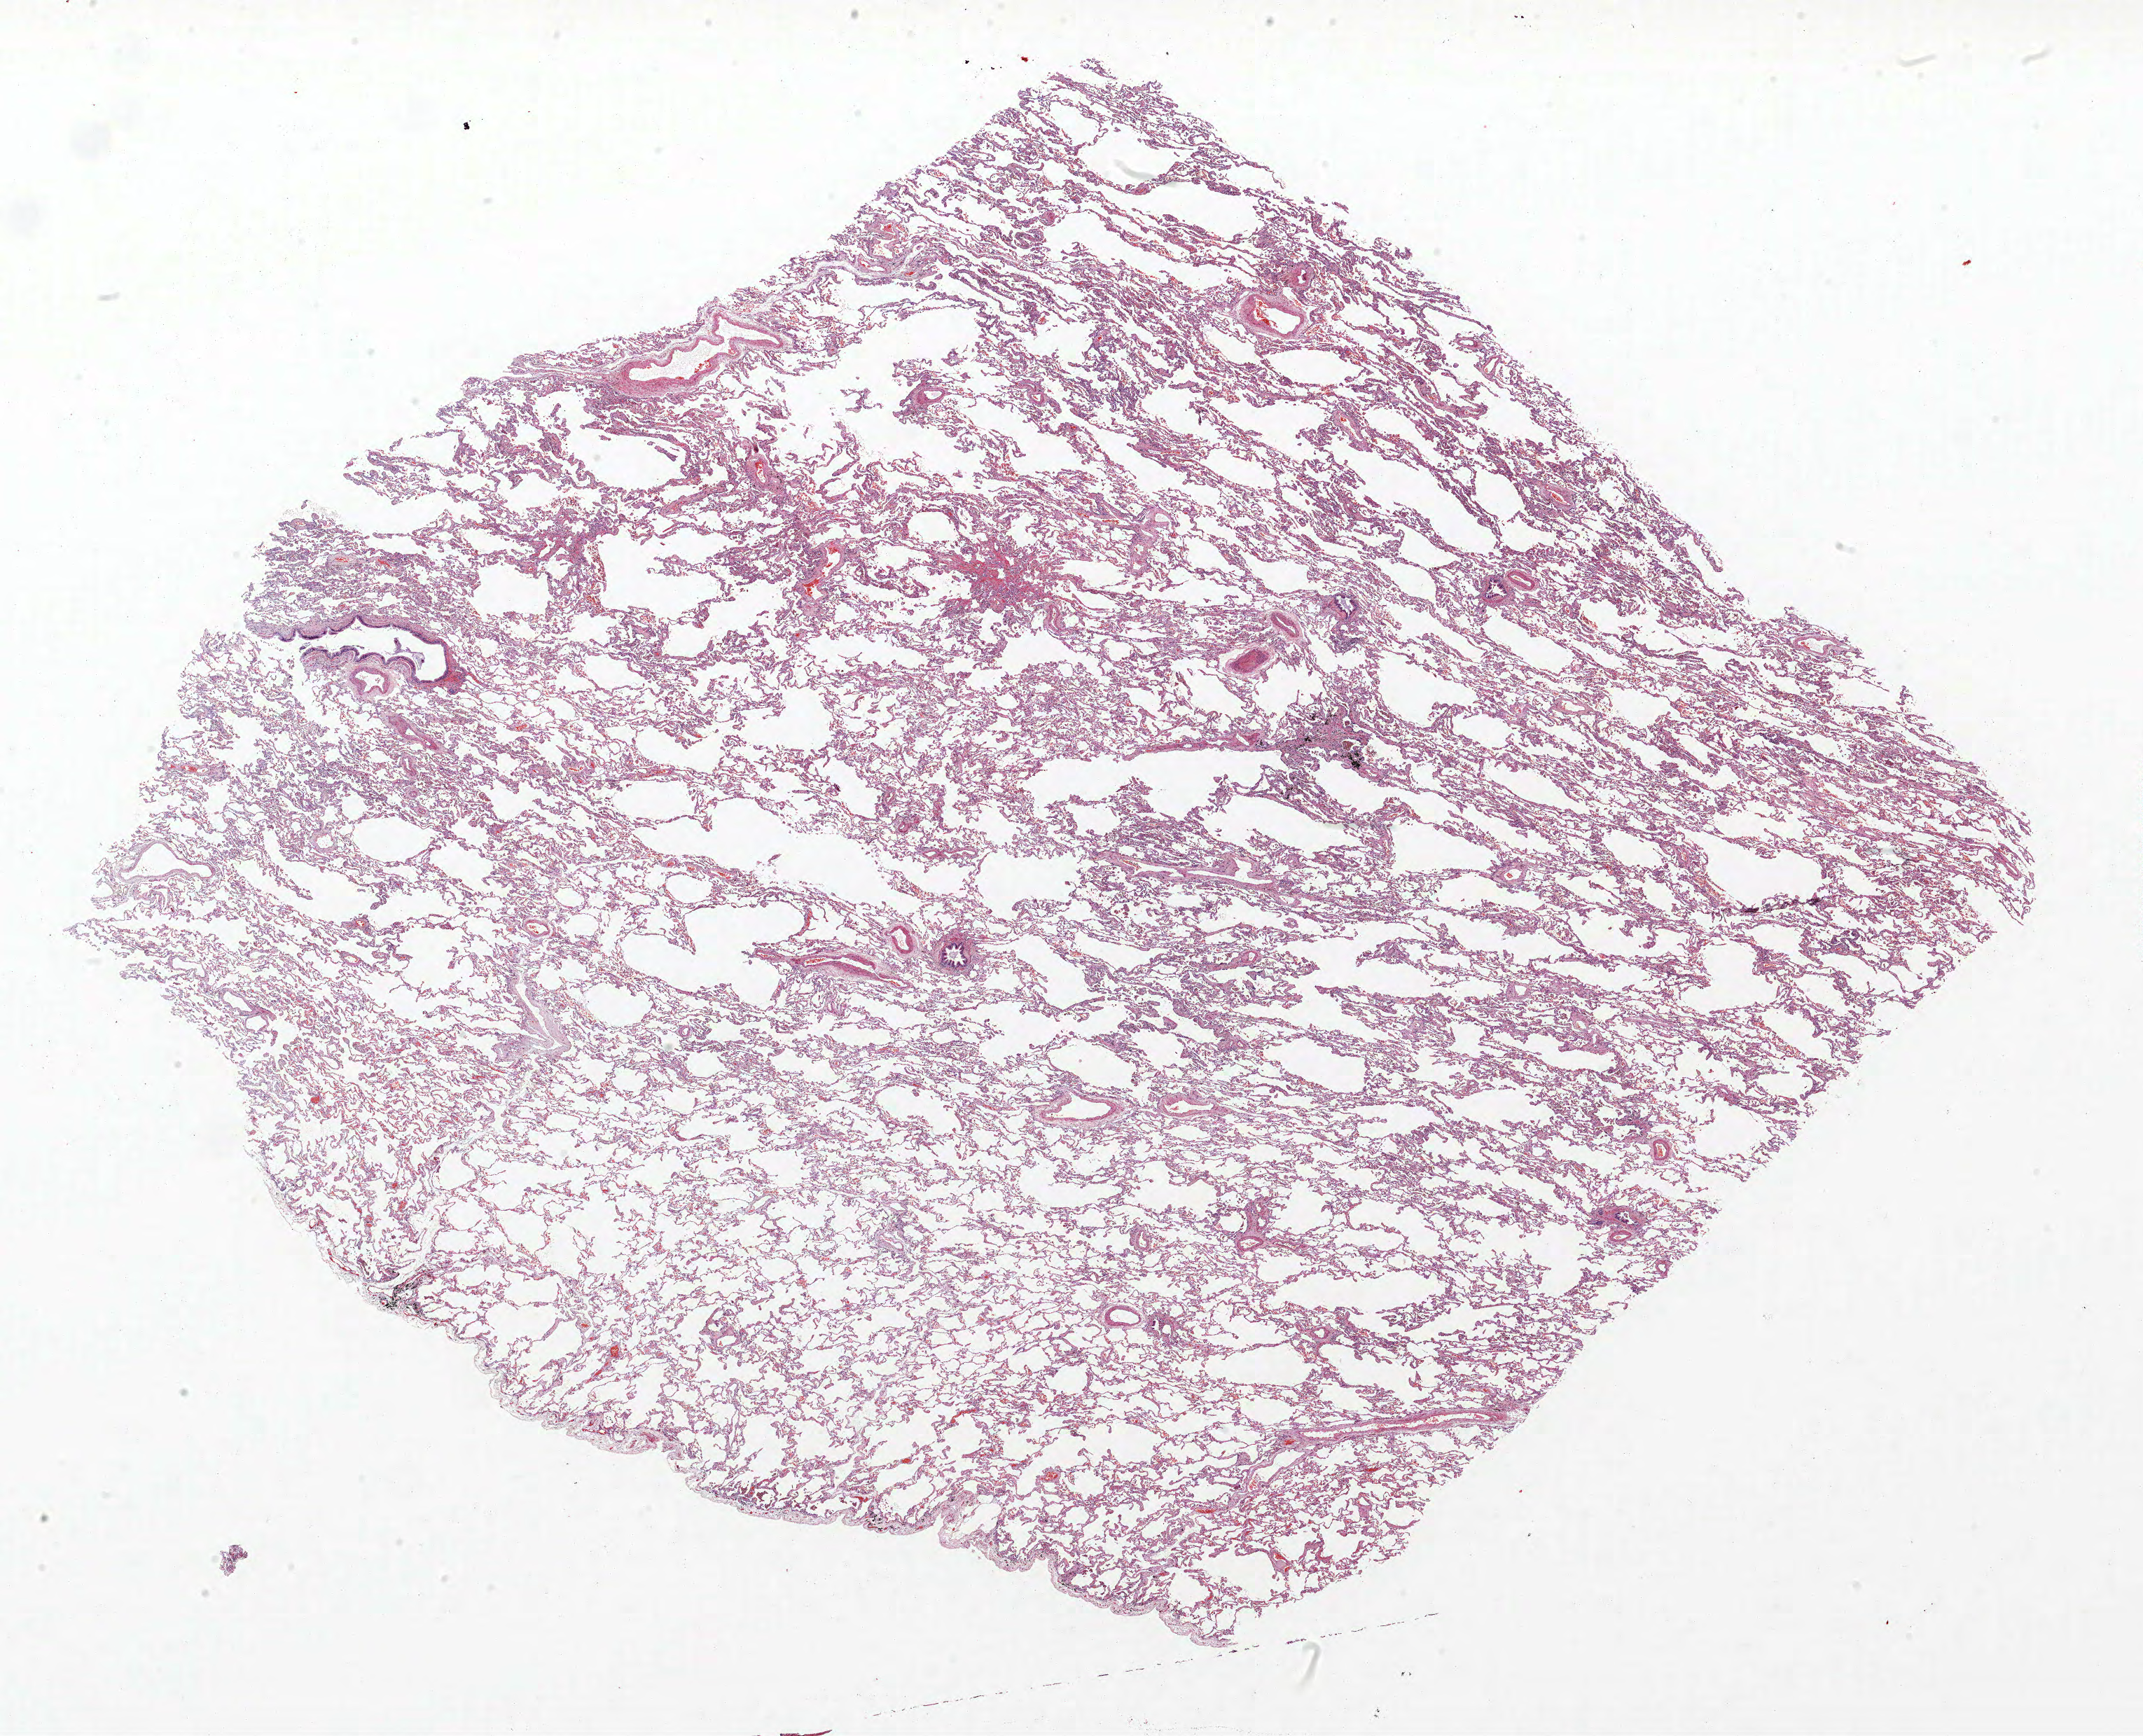
Whole-slide histology image, H&E-stained, low-resolution overview of the scanned area, about 24.5 x 19.8 mm (slide scanned at 40x), formalin-fixed paraffin-embedded (FFPE) section, lung tissue. Female, age 64 at enrolment. Current smoker at enrolment.
• stage (AJCC 6th edition): IA
• tumour size (pathology): 12 mm
• primary tumour location (clinical record): right upper lobe
• participant's lung-cancer diagnosis: Large cell neuroendocrine carcinoma (ICD-O-3 8013/3)